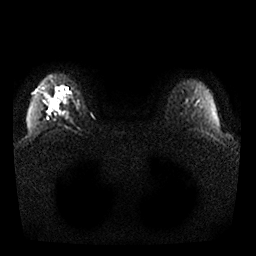
Breast MRI, one axial slice. Position 21 of 25 along the scan axis. Diffusion-weighted series; image 2 of 4 stored at this slice position (different b-values; order by instance number). 1.5 T. 4 mm slice thickness. 256 × 256 image matrix, field of view 350 × 350 mm. Female patient.
Outlined on this slice (expert manual segmentation):
- tumour on diffusion-weighted imaging: bounding box [x1, y1, x2, y2] px = [47, 99, 50, 104]